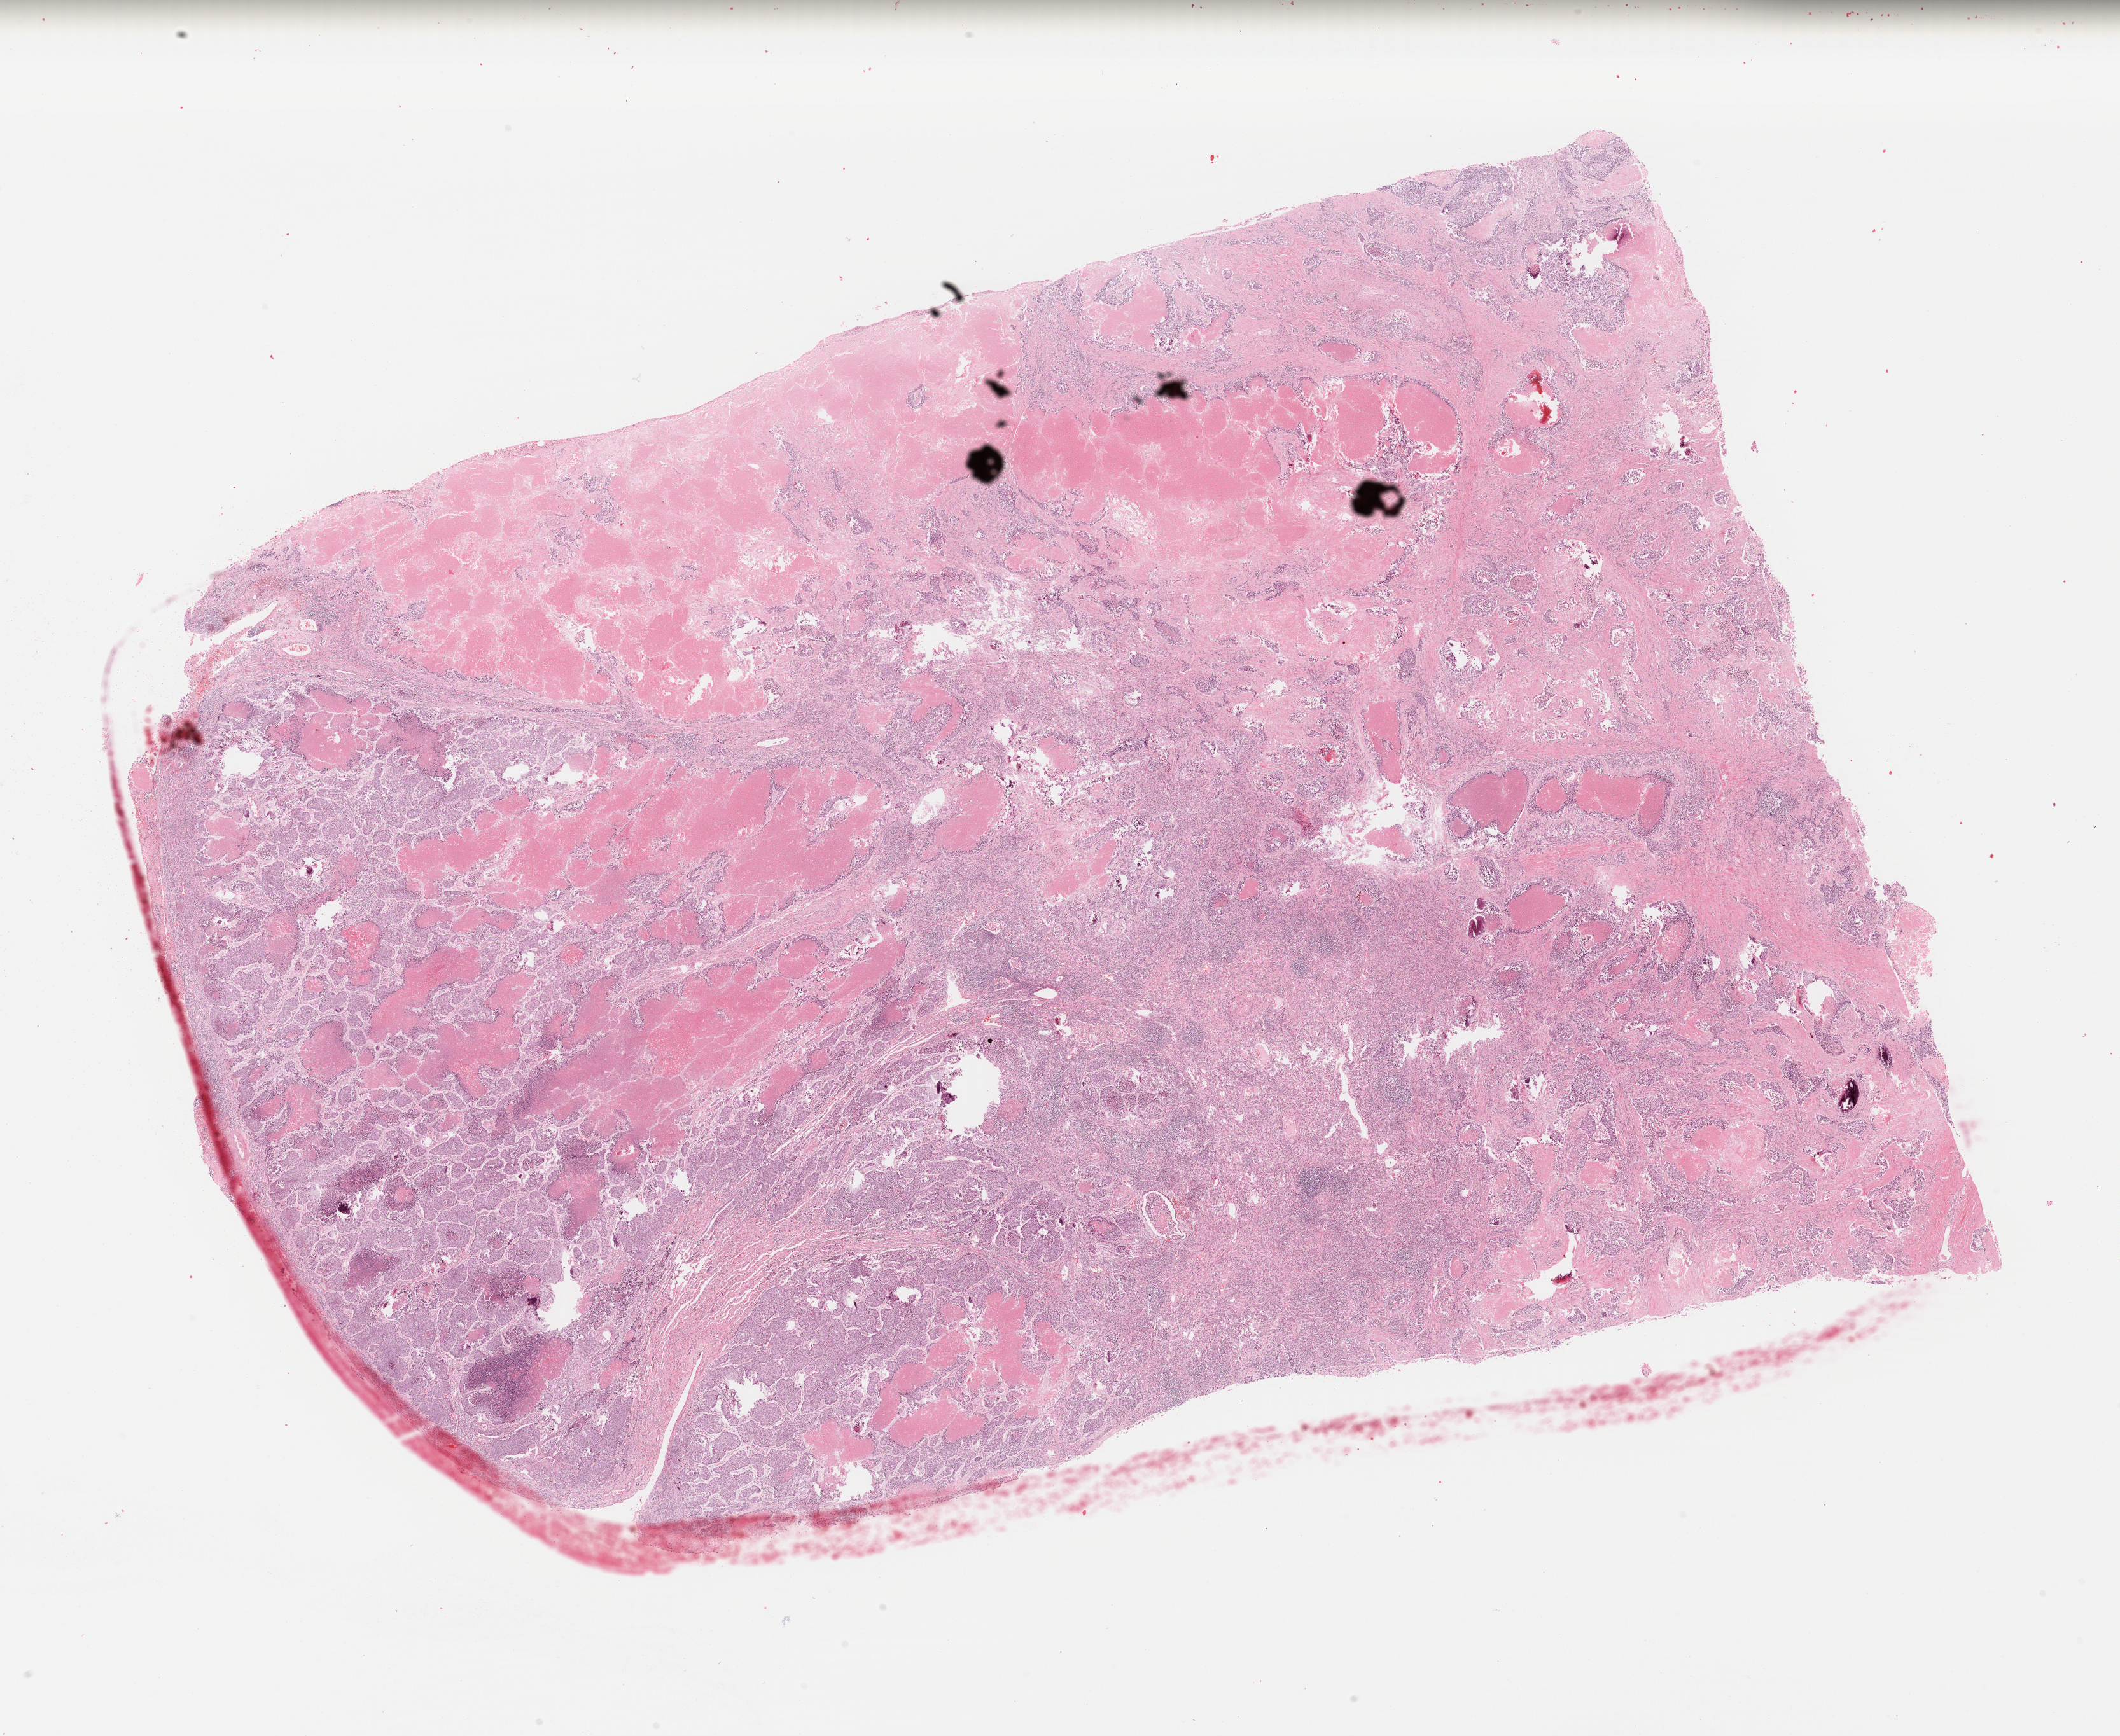
Whole-slide histology image, H&E-stained — a low-resolution overview of the entire scanned area, about 26.2 x 21.4 mm (slide scanned at 40x); formalin-fixed paraffin-embedded (FFPE) diagnostic section; lung, primary tumour sample. Female patient; age at initial diagnosis 74 years.
Laterality: left. AJCC pathologic stage: IIB (7th edition). Diagnosis: Squamous cell carcinoma, NOS (lower lobe, lung).